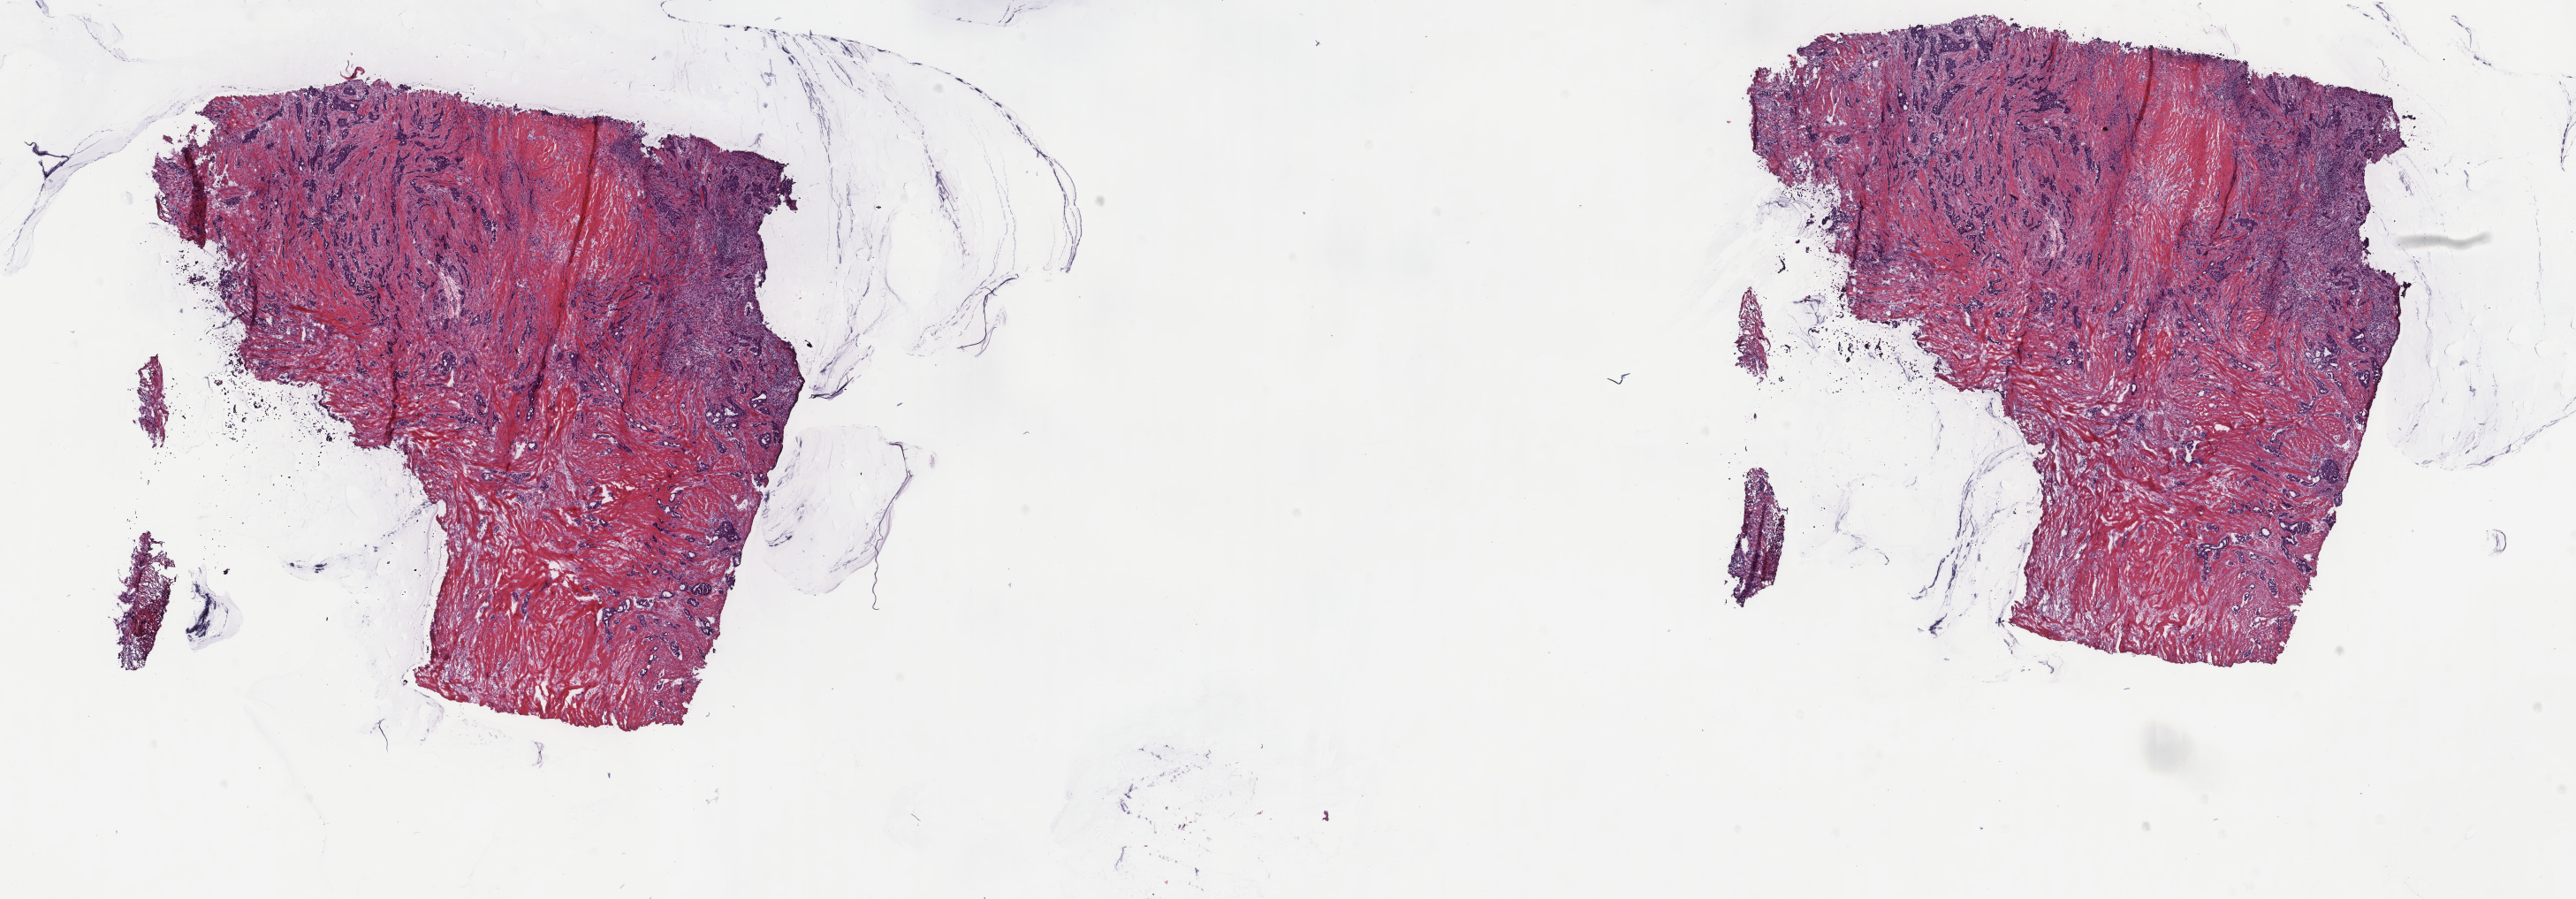
Digitized H&E tissue section (whole slide), low-resolution overview of the scanned area, about 23.1 x 8.1 mm (slide scanned at 40x); frozen section; primary tumour sample from the breast. Female patient; age at initial diagnosis 84 years. Slide review estimates, as recorded: tumour cells 60%, tumour nuclei 65%, normal cells 0%, stromal cells 40%, necrosis 0%. Infiltration values recorded for this section: lymphocyte infiltration 2%, monocyte infiltration 0%, neutrophil infiltration 0%.
- AJCC pathologic stage: IIA
- histologic diagnosis: Infiltrating duct carcinoma, NOS
- lymph nodes positive (case pathology): 0 of 8 examined
- laterality: left